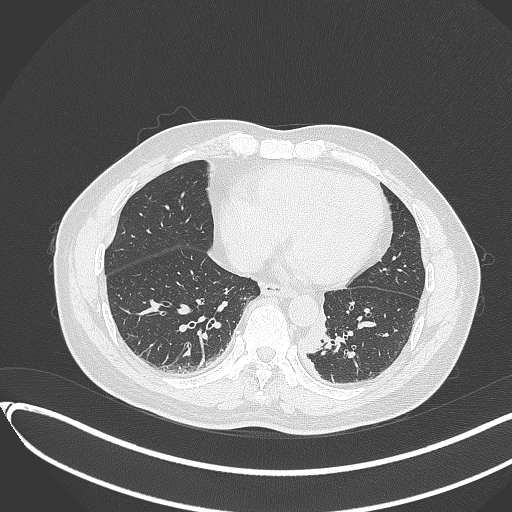
Chest CT, one axial slice. Reconstruction kernel B70f. 120 kVp. Lung window (W 1500 / L -600 HU). 1 mm slice thickness. 512 × 512 image matrix. Male patient, age 54 years. Case-level facts recorded for this patient, not image findings: clinical TNM (as recorded): T3 N0 M0.
Structures marked on this image (bounding box drawn by a radiologist):
- lung tumour (recorded histology: squamous cell carcinoma): bounding box (x1, y1, x2, y2) in pixels: (301, 303, 331, 356)